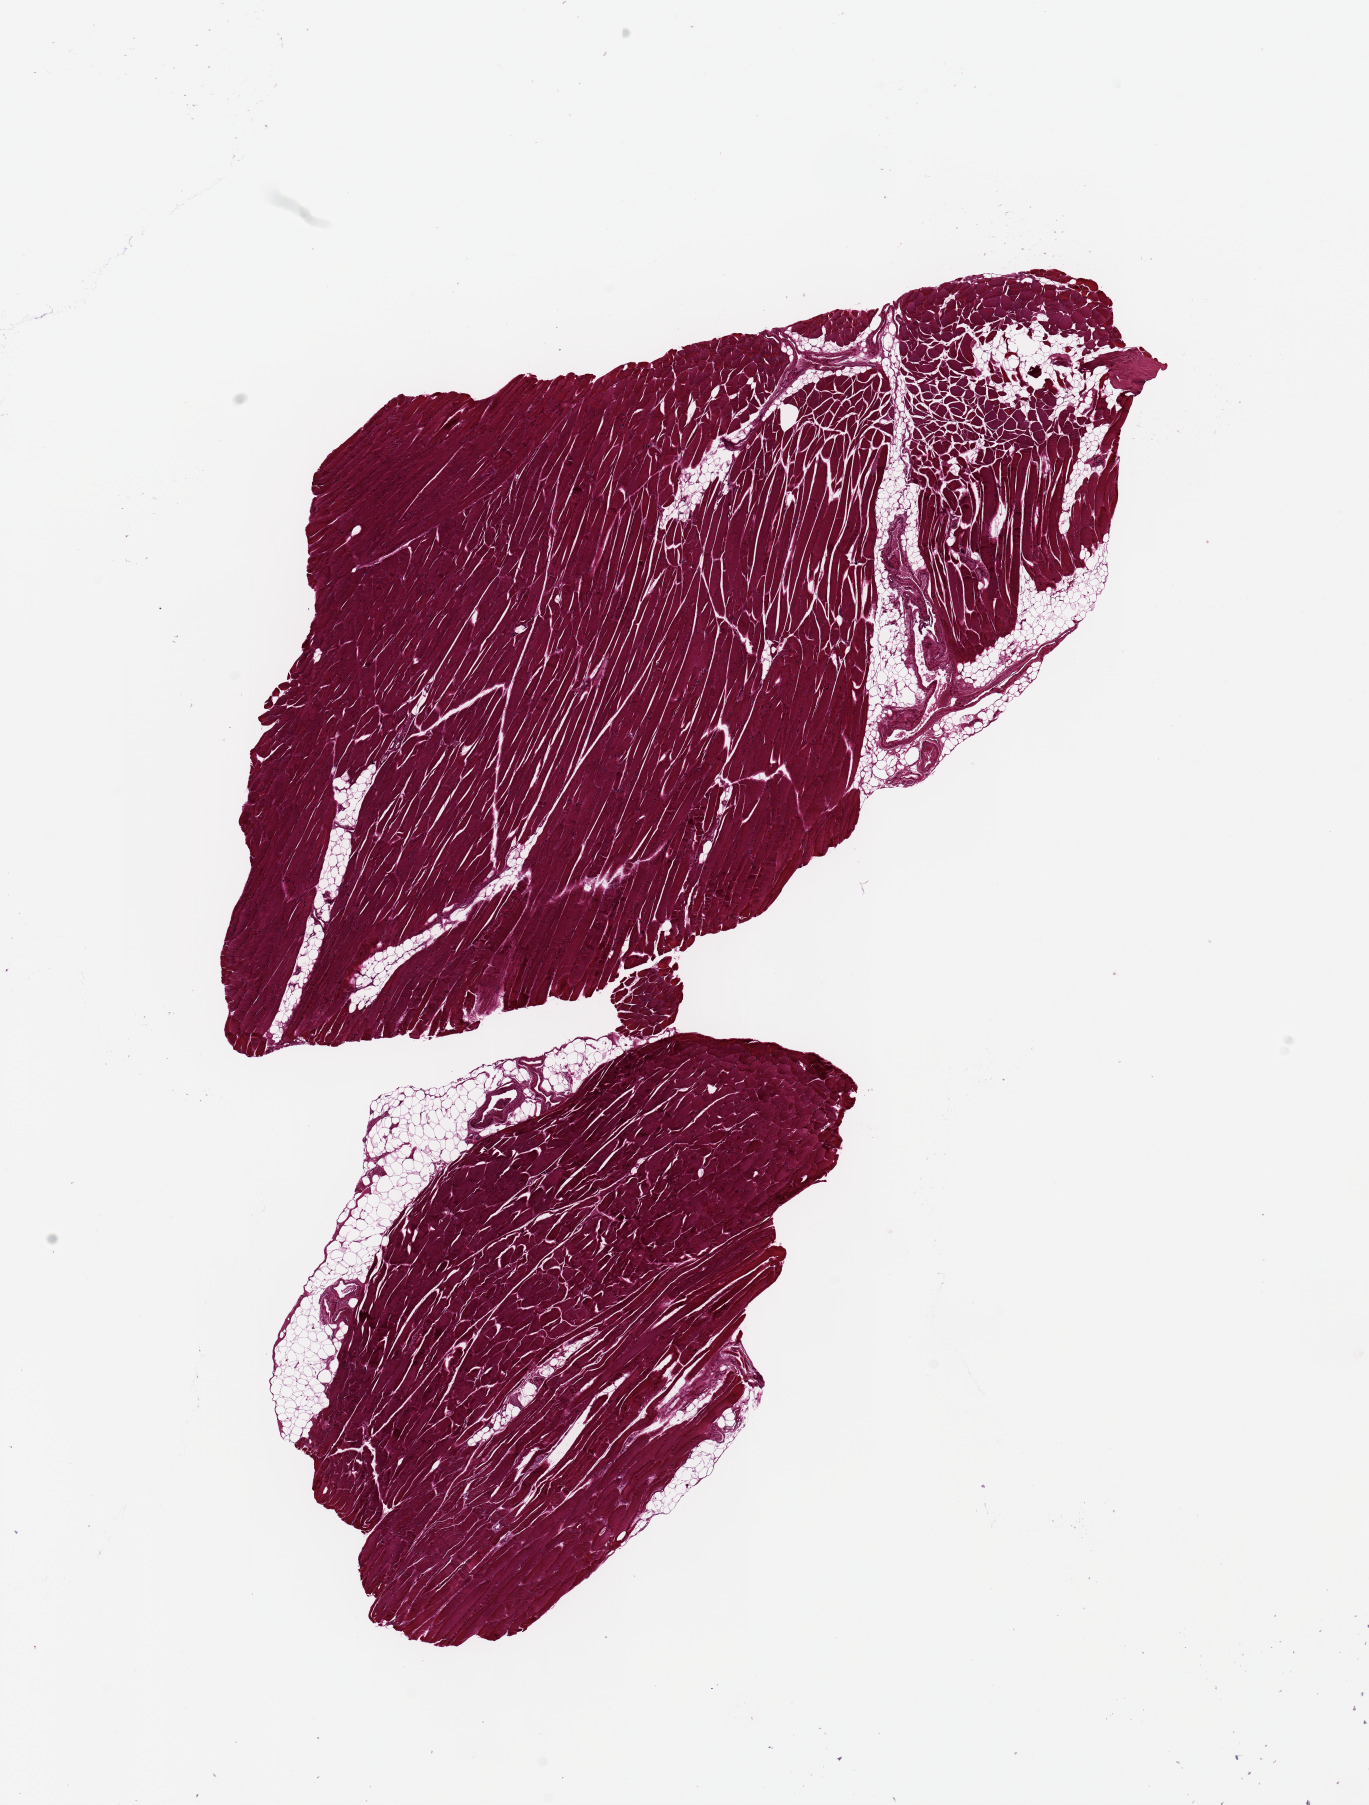
Whole-slide image, hematoxylin and eosin (H&E) stain, whole scanned area (about 10.8 x 14.3 mm, from a 20x scan) shown as a low-resolution overview, PAXgene-fixed, paraffin-embedded tissue, section of skeletal muscle (target tissue), donor tissue sample. Donor sex: female.
Pathologist's review note for this sample: 7.4x 4.5mm & 5.3x3.4mm. Sparse interfibrillar fat, a few foci of which are under fixed.